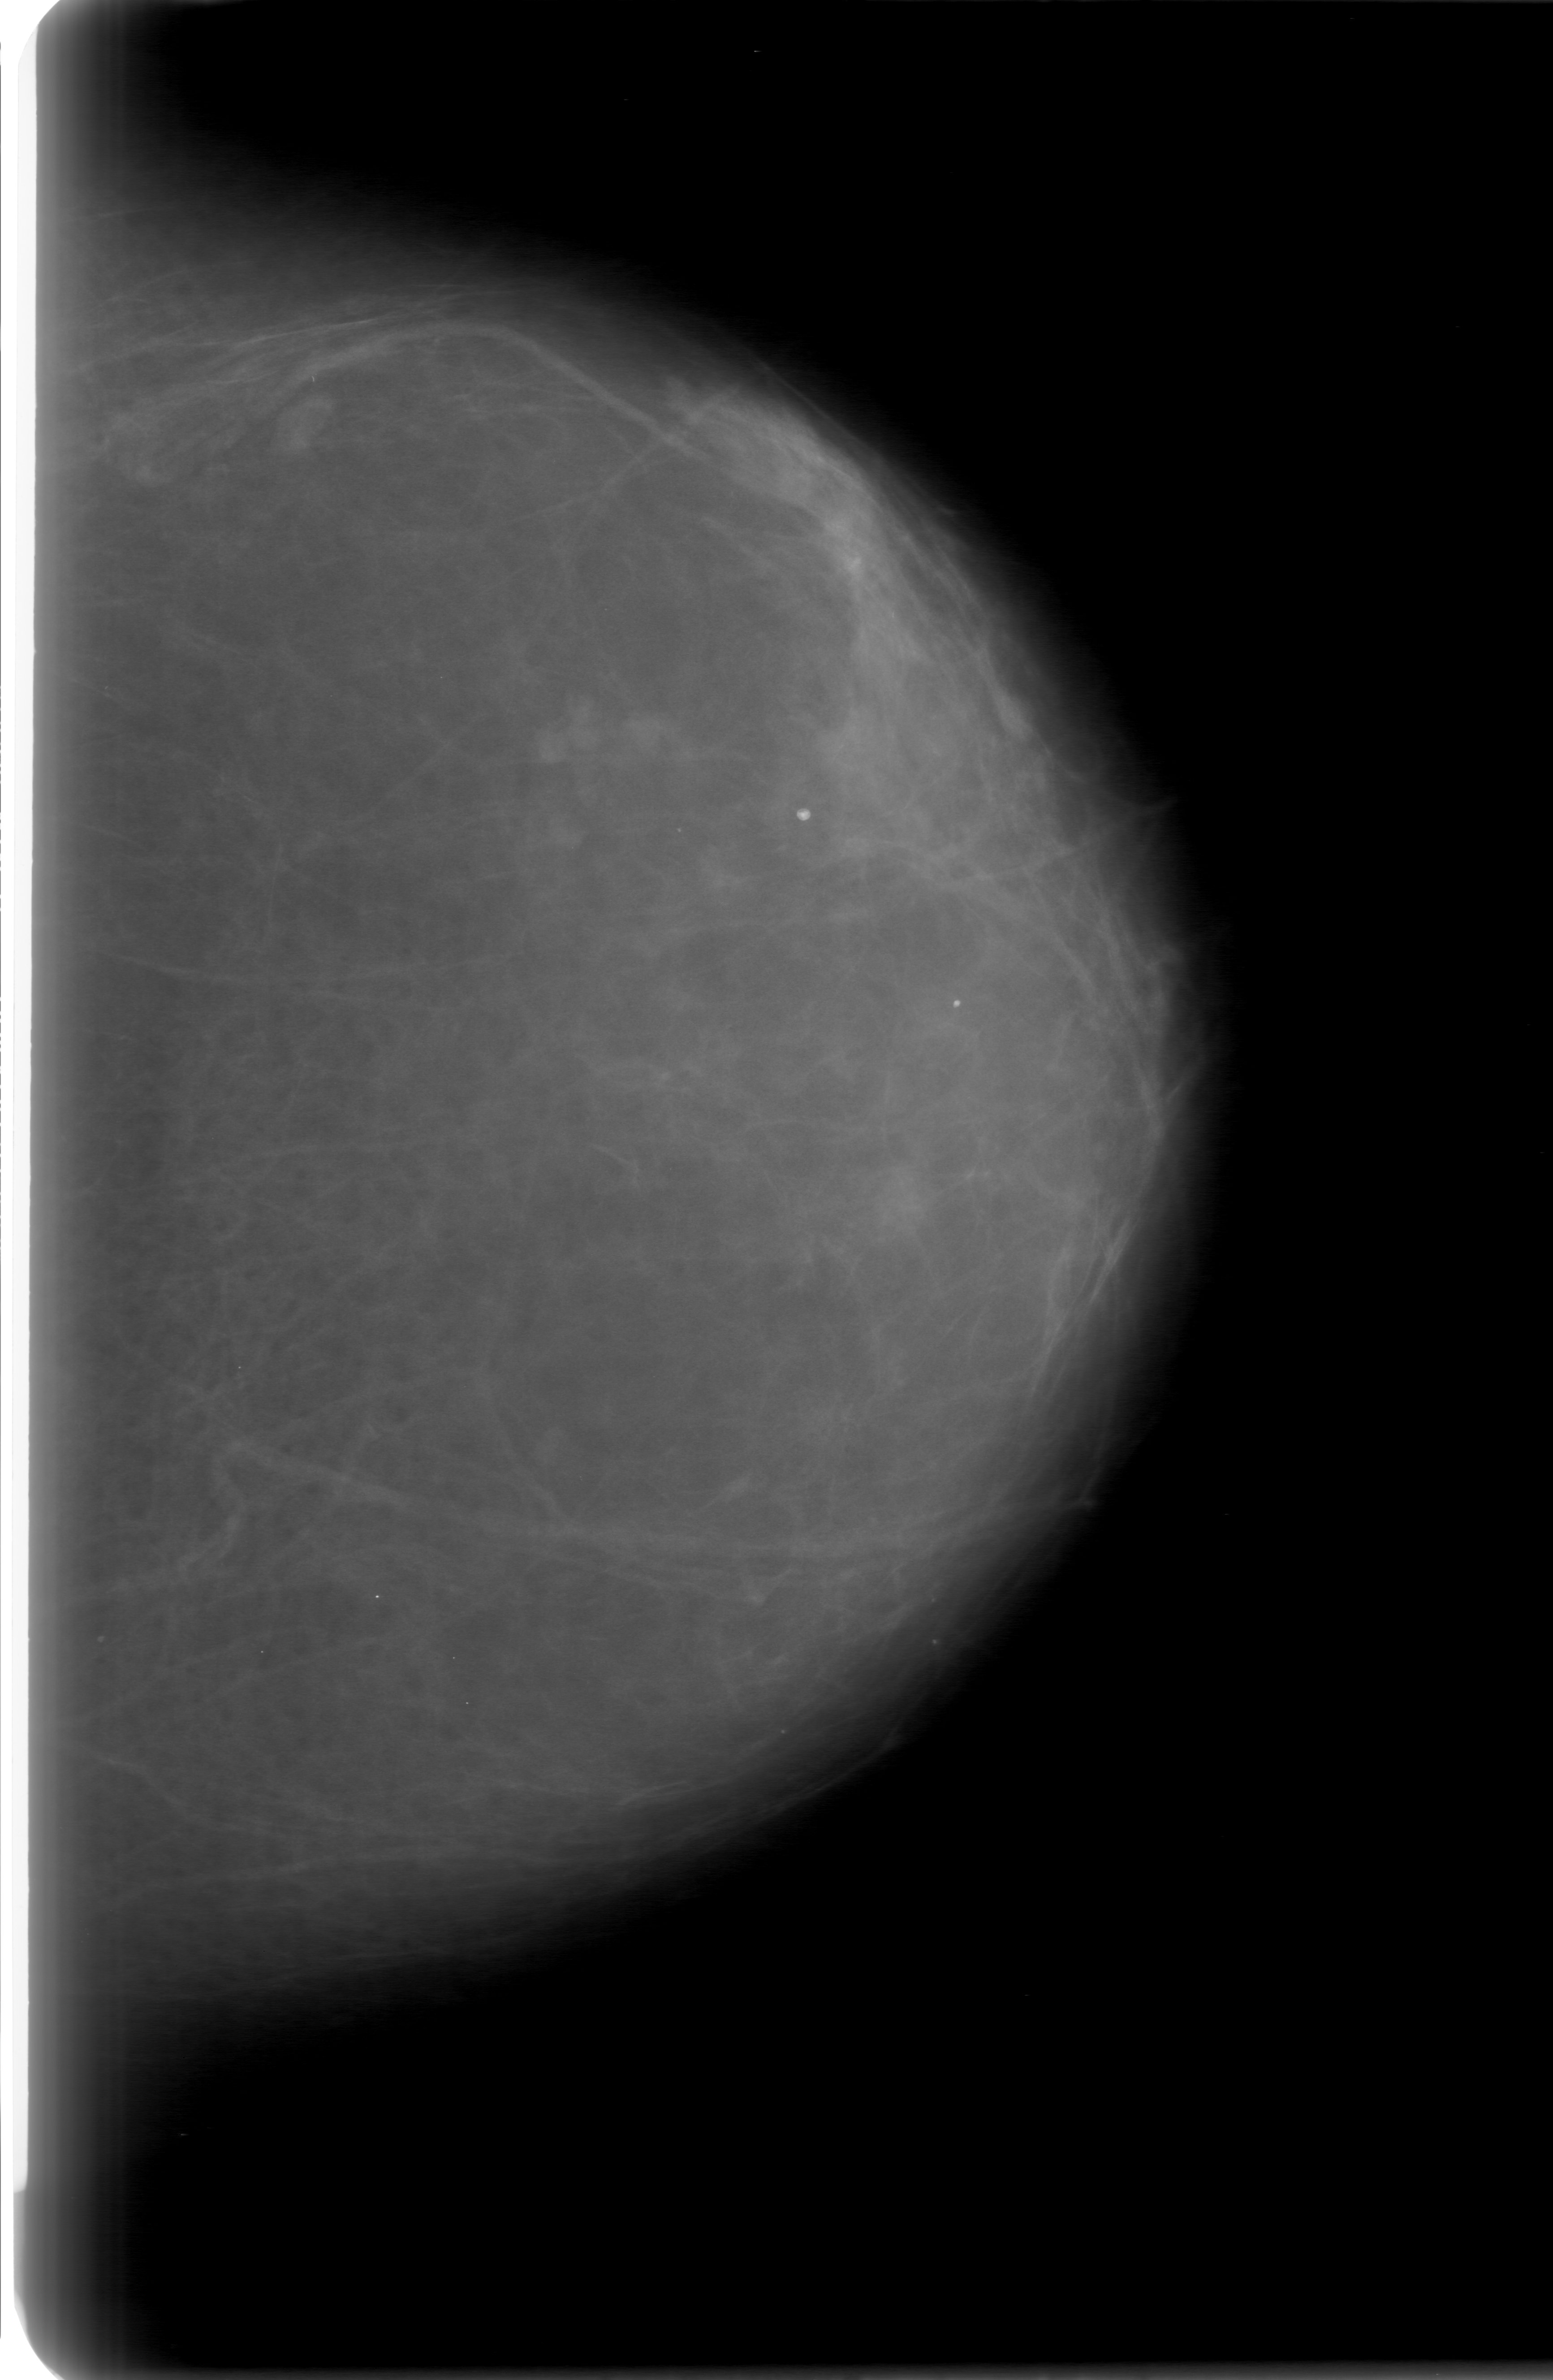
Digitized screen-film mammogram; left breast; craniocaudal (CC) view; breast composition: almost entirely fatty (BI-RADS density category 1 of 4).
Marked findings (only marked abnormalities are described; nothing is implied about the rest of the image): mass, shape lobulated, margins obscured; BI-RADS assessment category 0 (incomplete: needs additional imaging); pathology (as recorded): benign.